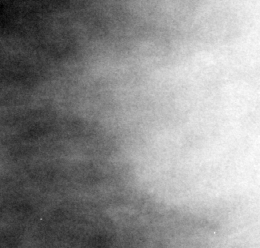
Region of interest cut from a scanned film mammogram (one marked finding); right breast; MLO view.
Marked abnormality: mass, shape irregular, margins microlobulated; BI-RADS assessment category 5; subtlety rating 5 on a 1 (subtle) to 5 (obvious) scale; pathology result (as recorded, not read from the image): malignant.